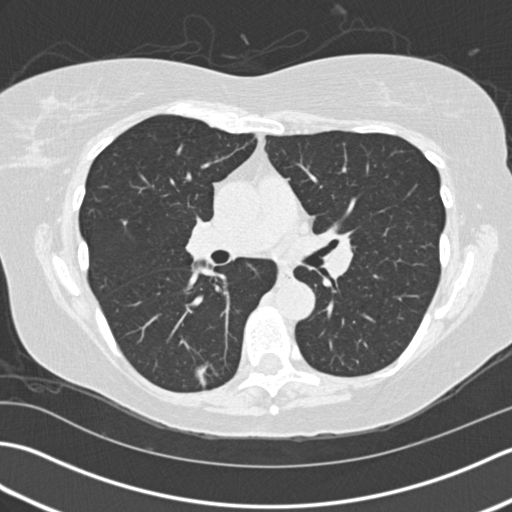
Axial slice from a low-dose chest CT screening exam; third screening round (two years after baseline); lung window (W 1500 / L -600 HU); 2 mm slice thickness. Female, age 60 years at enrolment. Former smoker at enrolment.
- Expert reader's lesion annotation, bounding box (x1, y1, x2, y2) in pixels: (182, 351, 229, 394).
- The screening reader recorded 3 non-calcified nodules or masses ≥4 mm on this exam (right lower lobe, right middle lobe, right middle lobe); which of them this box marks is not recorded.
- Later outcome: lung cancer diagnosed 68 days after this screen — acinar cell carcinoma, right lower lobe, moderately differentiated (G2), stage IA (AJCC 6th edition), 10 mm at pathology.